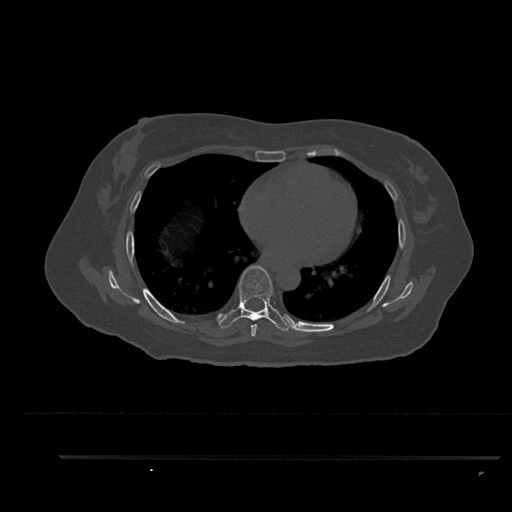
CT including the spine, one axial slice. Slice 518 of 797 in the series (ordered by position). Bone window (W 1800 / L 400 HU). 0.5 mm slice thickness. 512 × 512 image matrix, field of view 408 × 408 mm. Female patient, age 44 years. From the clinical record (not read from this slice): primary cancer: renal.
Structures marked on this image (semi-automatic segmentation, software-assisted and operator-edited):
- T6 vertebra: bounding box (x1, y1, x2, y2) in pixels: (251, 320, 257, 337)
- T7 vertebra: (219, 266, 296, 331)